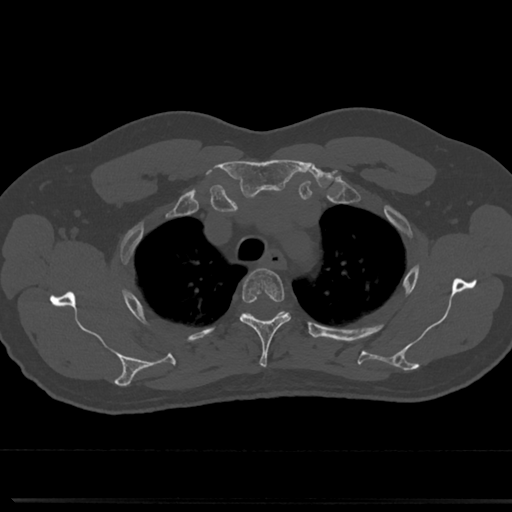
CT including the spine, one axial slice; position 584 of 817 along the scan axis; bone window (W 1800 / L 400 HU); 0.5 mm slice thickness; 512 × 512 image matrix. Patient: male, 61 years. From the clinical record (not read from this slice): primary cancer: prostate.
Annotated regions visible in this slice (semi-automatically segmented with operator editing):
- T3 vertebra: bounding box (x1, y1, x2, y2) in pixels: (239, 270, 291, 369)
- T4 vertebra: (242, 310, 307, 340)